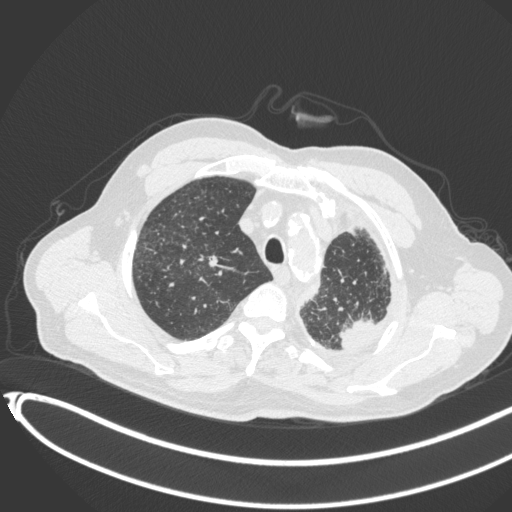
Chest CT, one axial slice. Slice 353 of 451 in the series (ordered by position). Lung window (W 1500 / L -600 HU). 1 mm slice thickness. 512 × 512 image matrix. Patient: male, 78 years. From the clinical record (not read from this slice): clinical TNM (as recorded): T1c N0 M1.
Outlined on this slice (rectangle marked by the reading radiologist):
- lung tumour (recorded histology: adenocarcinoma): bounding box <336,316,388,357> (left, top, right, bottom; pixels)